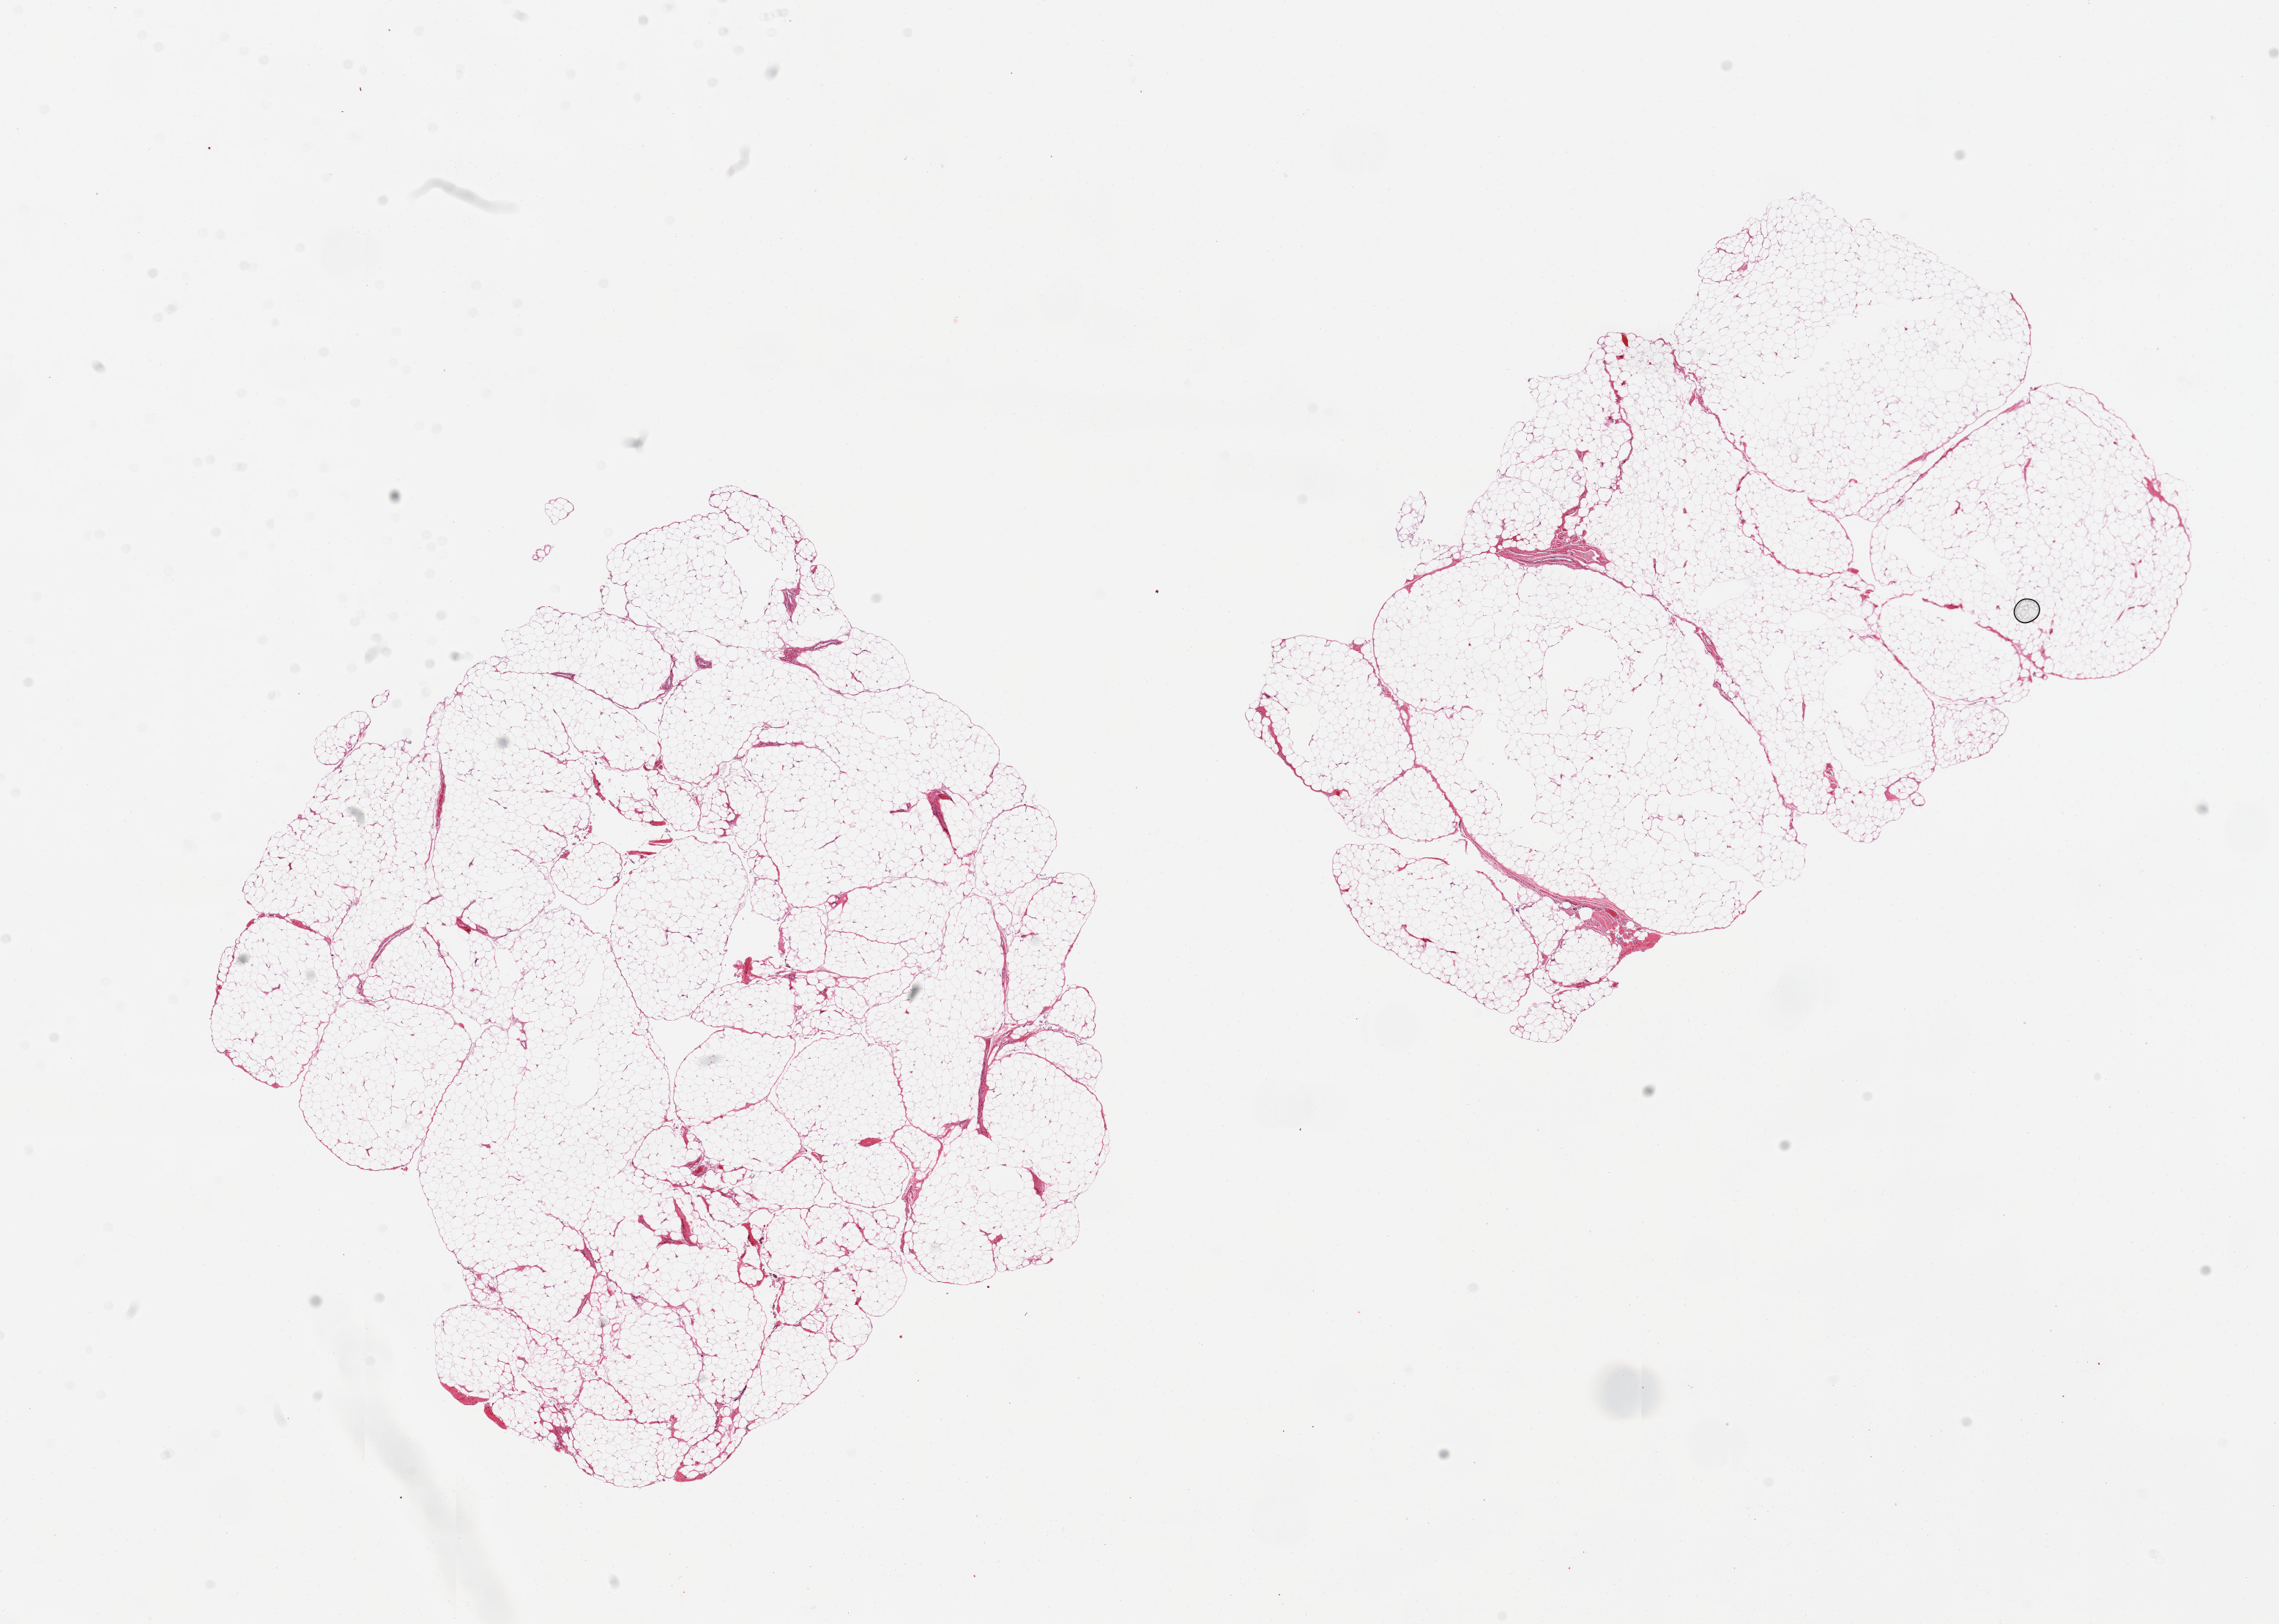
Haematoxylin and eosin whole-slide image — a low-resolution overview of the entire scanned area, about 24.6 x 17.5 mm, PAXgene-fixed paraffin-embedded (PFPE) section, sampled site (target tissue): omentum, donor tissue sample. Donor: male.
* review note (as recorded): 2 pieces, ~5% interstital fibrosis